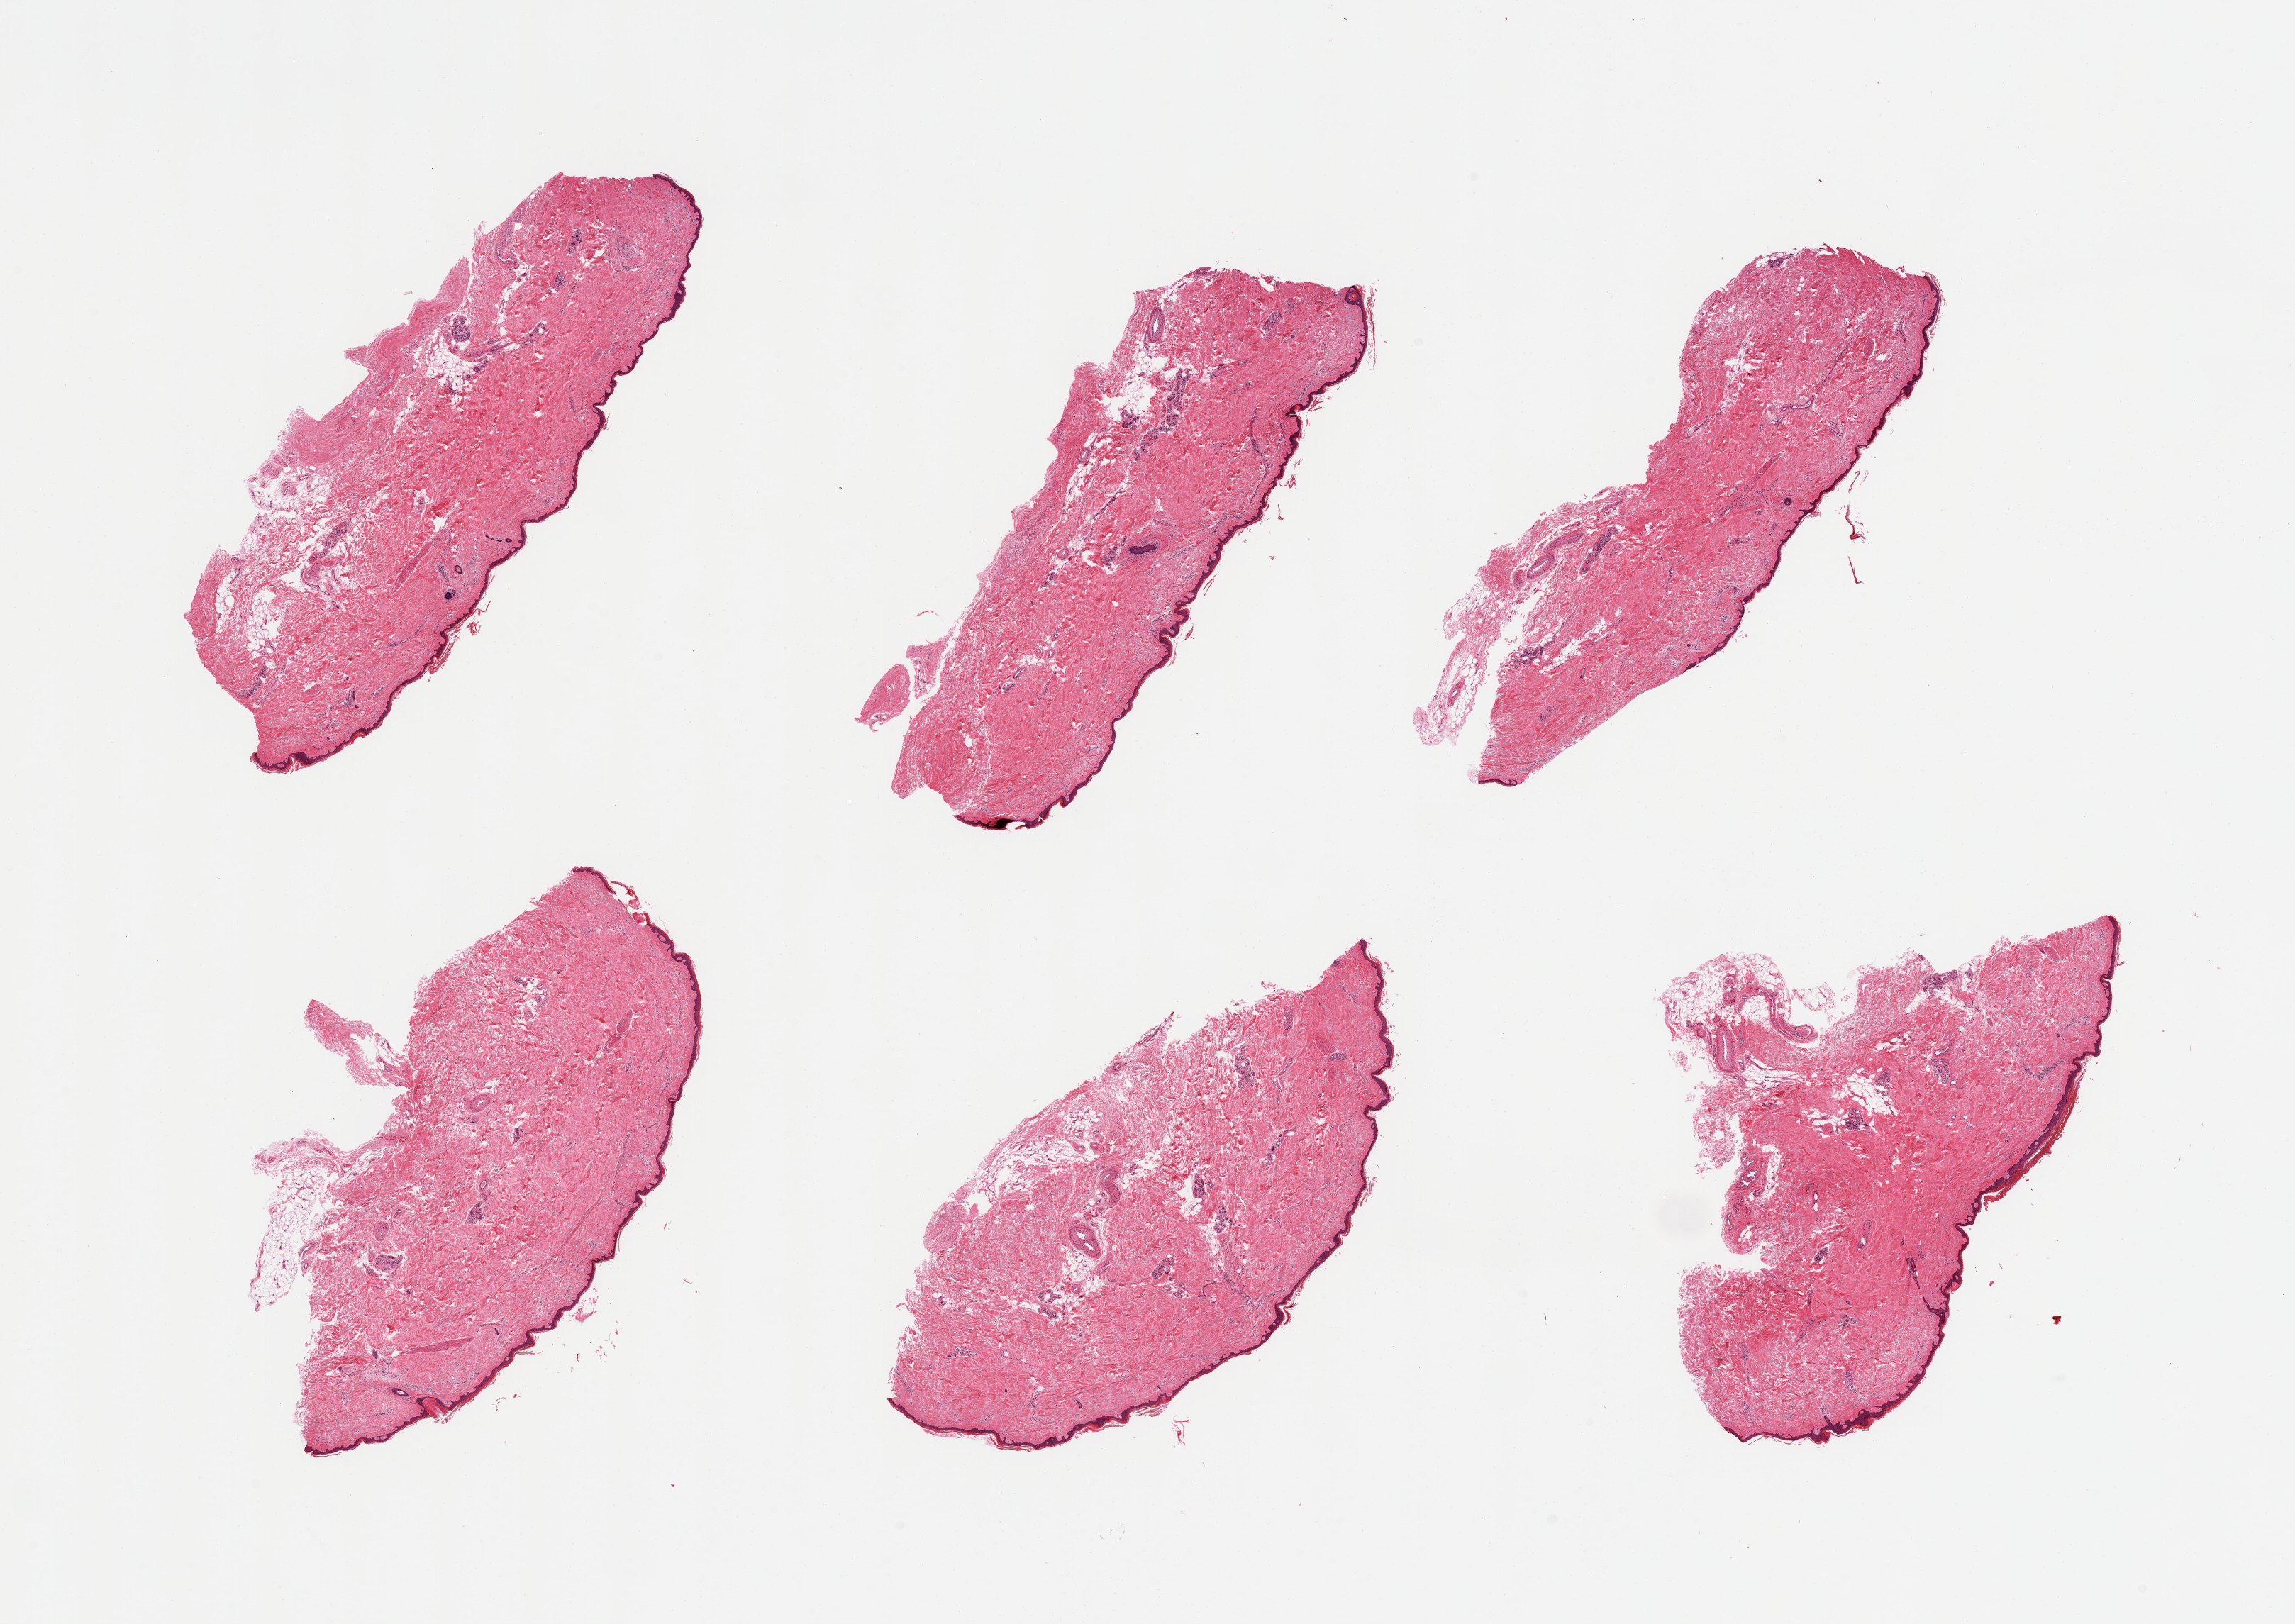
Digitized haematoxylin and eosin-stained section — shown as a low-resolution overview of the whole scanned area (about 25.6 x 18.1 mm, from a 20x scan). PAXgene-fixed paraffin-embedded (PFPE) section. Target tissue: skin of lower leg. Tissue donor sample. Donor sex: male.
* review note (as recorded): 6 pieces; well trimmed; 10% dermal fat